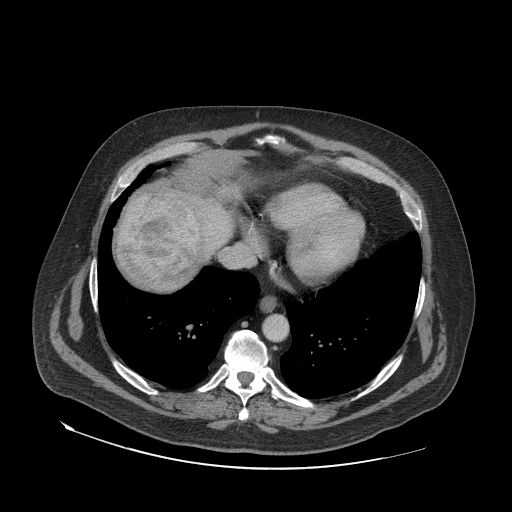
Contrast-enhanced abdominal CT (liver protocol), one axial slice; 140 kVp; soft-tissue window (W 400 / L 40 HU); 512 × 512 image matrix, field of view 480 × 480 mm. From the clinical record (not read from this slice): diagnosis: hepatocellular carcinoma (patient treated with transarterial chemoembolisation; whether this scan precedes or follows treatment is not stated here); TNM stage (as recorded): Stage-IVA; Child-Pugh class: A.
Structures marked on this image (semi-automatically segmented with operator editing):
- abdominal aorta: bounding box <264,315,287,339> (left, top, right, bottom; pixels)
- liver parenchyma outside the tumour (the mass and vessels are separate outlines, so this box may not span the whole liver): <118,188,232,290>
- mass: <120,190,201,284>